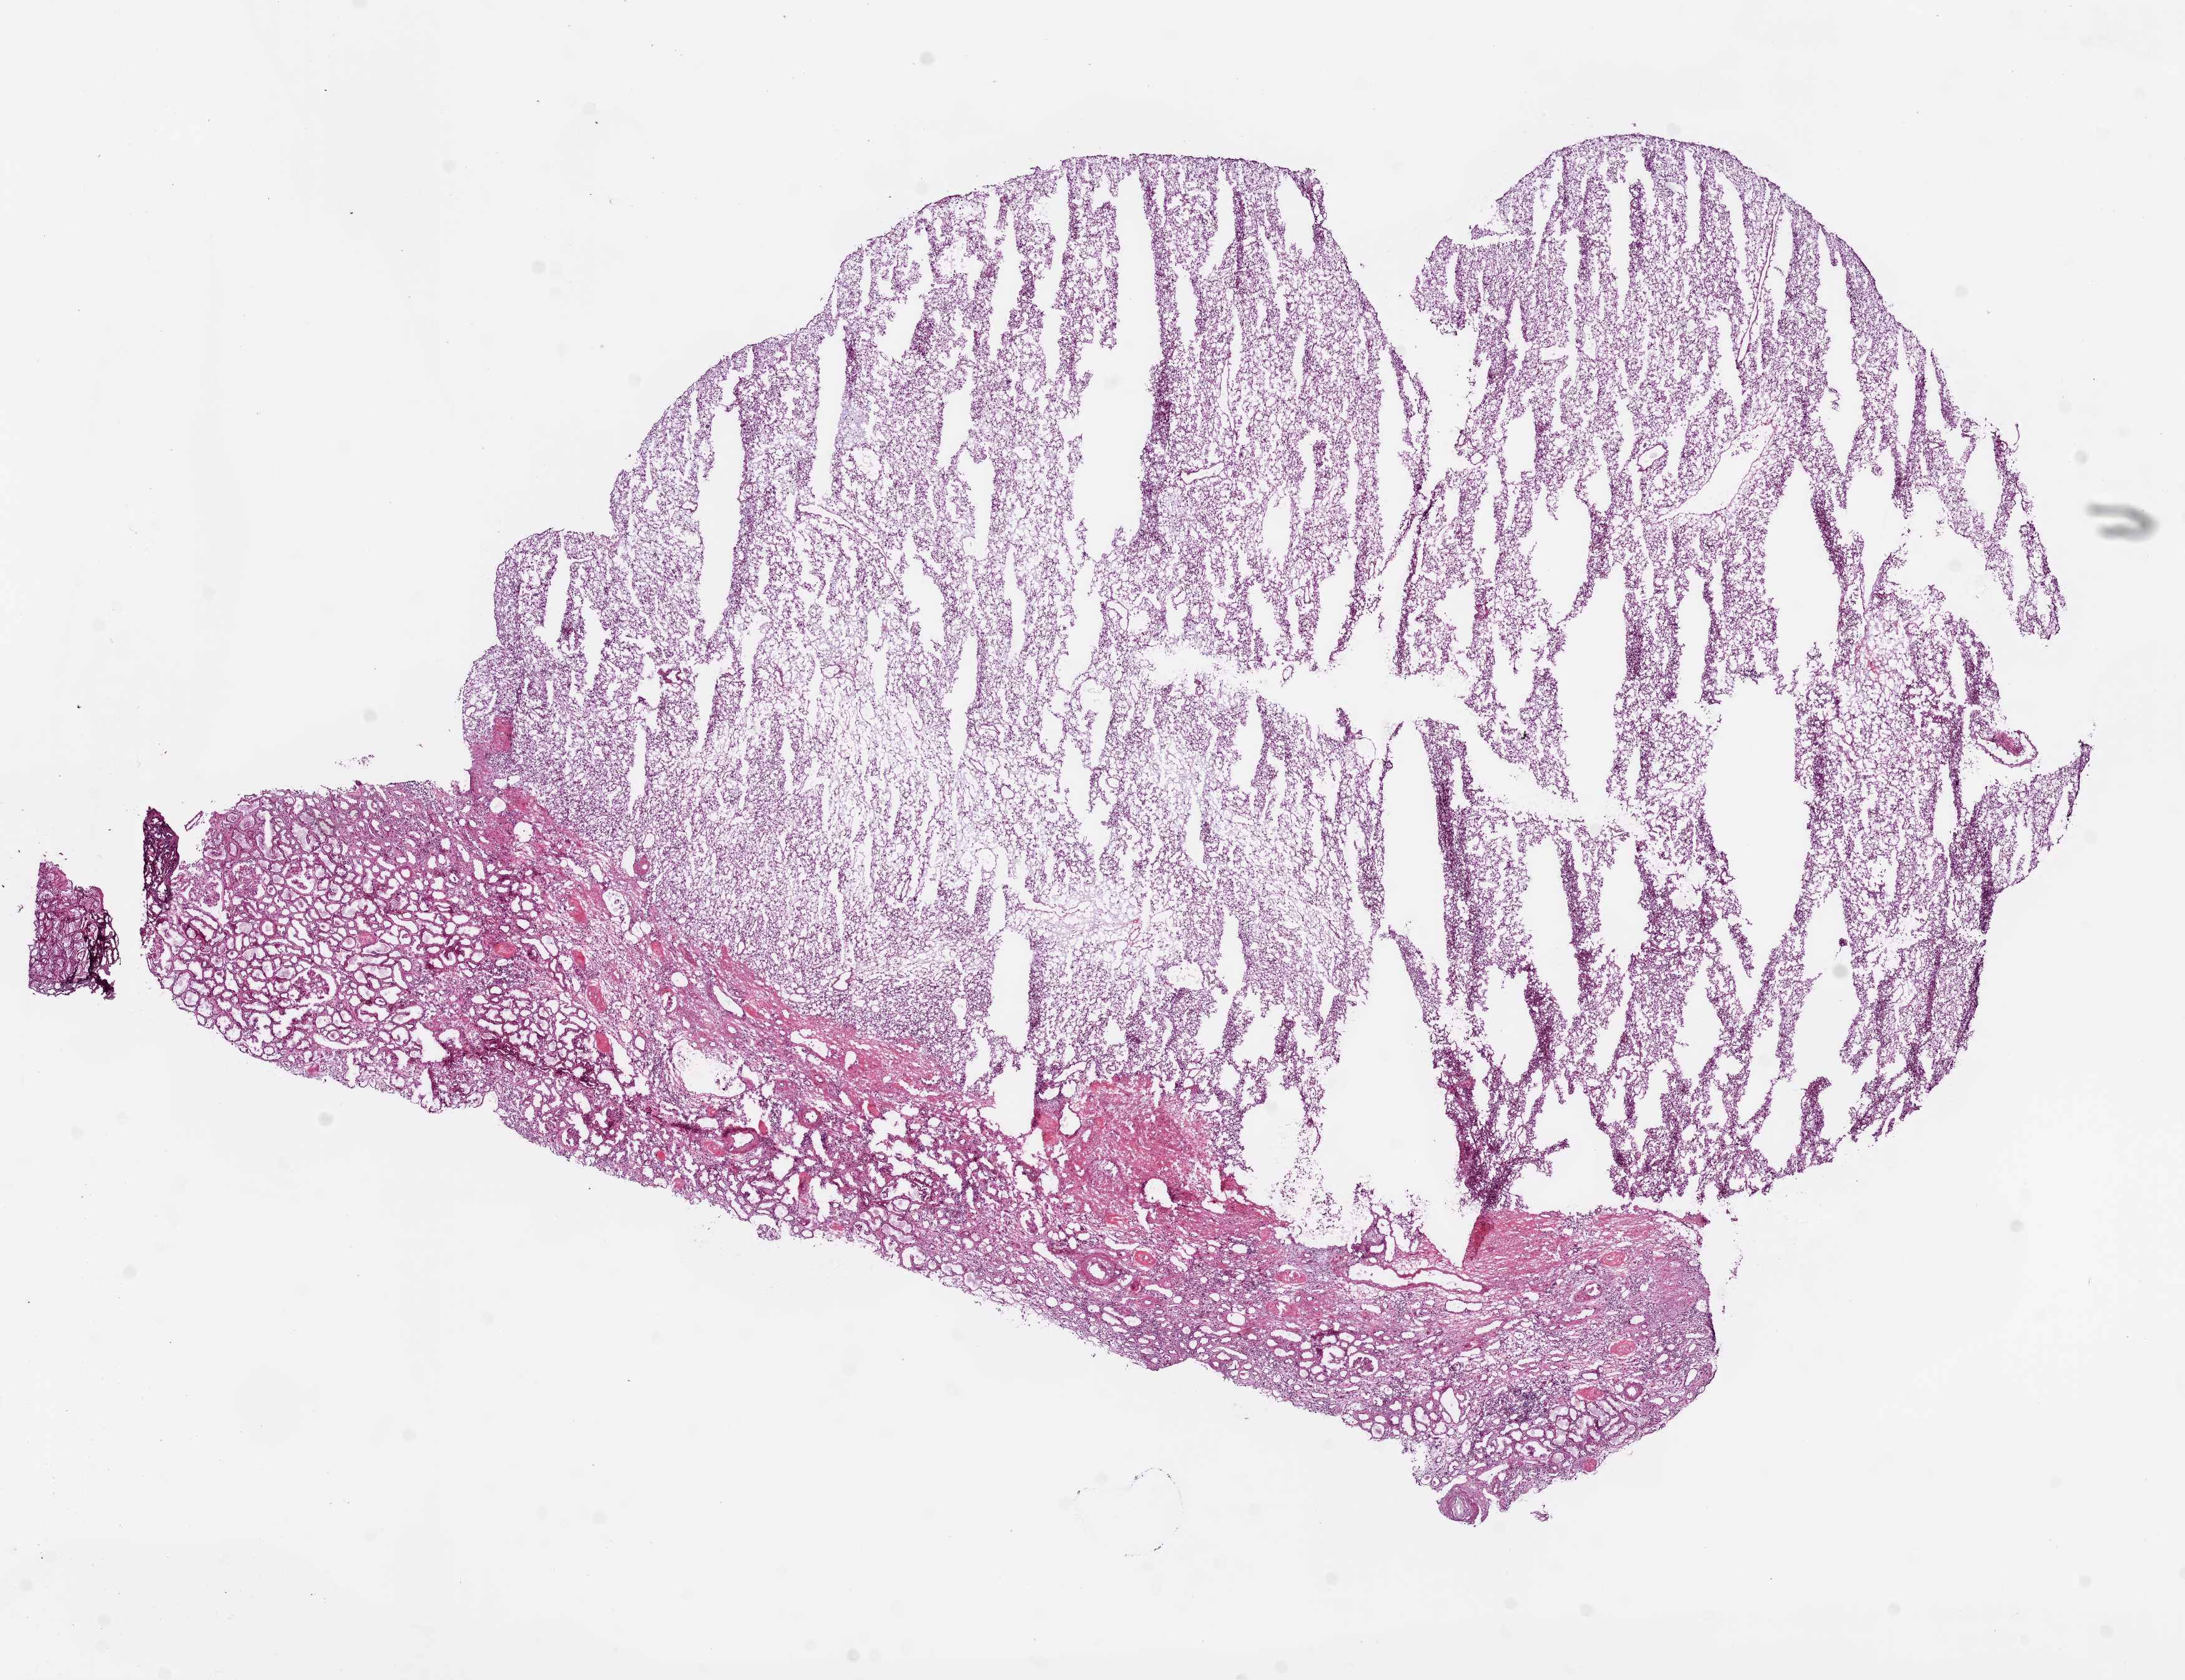
Hematoxylin and eosin (H&E) stained whole-slide image, a low-resolution overview of the entire scanned area, about 14.0 x 10.8 mm (acquisition: 20x scan), frozen section from the bottom of the tissue portion, primary tumour sample from the kidney. Patient: female, age at initial diagnosis 79 years. Histologic grade: G2 (moderately differentiated). Slide review estimates, as recorded: tumour cells 76%, tumour nuclei 75%, normal cells 24%, necrosis 0%. Inflammatory infiltration, as recorded: lymphocyte infiltration 1%.
Diagnosis: Clear cell adenocarcinoma, NOS. AJCC pathologic stage: I.